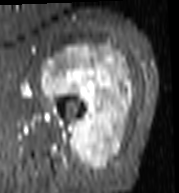
MRI of an extremity soft-tissue mass, one axial slice. Slice 74 of 103 in the series (ordered by position). STIR. MR volume resampled by the dataset authors to the PET/CT grid (not the native acquisition matrix). 3.27 mm slice thickness. 179 × 193 image matrix, field of view 175 × 188 mm. Female patient. Case-level facts recorded for this patient, not image findings: histological type: undifferentiated – high grade; grade: high; site of the primary tumour: left thigh.
Annotated regions visible in this slice (expert contour drawn on MRI and transferred to this co-registered scan by the dataset authors):
- gross tumour volume including surrounding oedema: box from (x=41, y=46) to (x=133, y=170) px
- gross tumour volume (mass): (x=41, y=46)–(x=133, y=170)